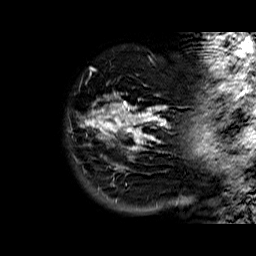
Breast MRI (dynamic contrast-enhanced), one sagittal slice. Slice 7 of 60 in the series (ordered by position). Dynamic contrast-enhanced series, time point 2 of 6 at this slice position (early post-contrast). 1.5 T. TE 6.3 ms, TR 32.4 ms. 256 × 256 image matrix, field of view 200 × 200 mm. Female patient. Case-level facts recorded for this patient, not image findings: setting: breast cancer imaged before/during neoadjuvant chemotherapy; receptor status: HR-positive, HER2-negative.
Outlined on this slice (semi-automatic segmentation, software-assisted and operator-edited):
- analysis volume of interest (the breast-tissue region the enhancement analysis was run in; not a lesion): bounding box [x1, y1, x2, y2] px = [80, 92, 176, 183]
- tumour enhancement mask (voxels above the 100 % enhancement threshold inside the analysis volume of interest): [80, 93, 166, 169]